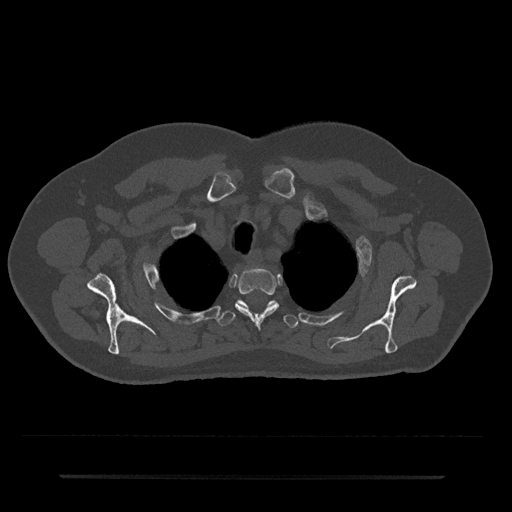
CT including the spine, one axial slice. Slice 594 of 797 in the series (ordered by position). 120 kVp. Bone window (W 1800 / L 400 HU). 0.5 mm slice thickness. 512 × 512 image matrix, field of view 437 × 437 mm. Patient: male, 69 years. From the clinical record (not read from this slice): primary cancer: prostate.
Outlined on this slice (semi-automatic segmentation, software-assisted and operator-edited):
- T2 vertebra: bounding box [x1, y1, x2, y2] px = [235, 268, 279, 324]
- T3 vertebra: [217, 300, 298, 328]